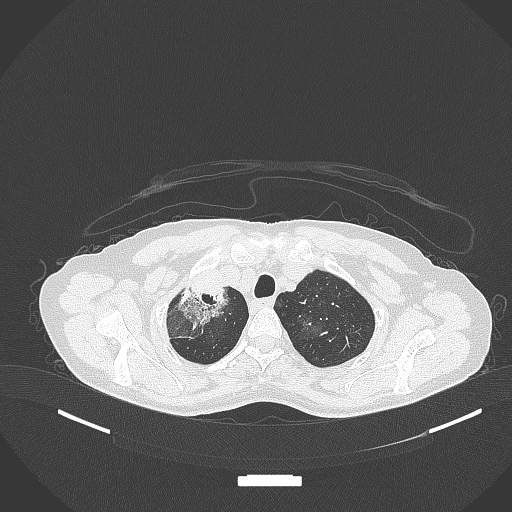
Chest CT, one axial slice; position 280 of 284 along the scan axis; reconstruction kernel B70f; lung window (W 1500 / L -600 HU); 512 × 512 image matrix. Female patient, age 59 years. Case-level facts recorded for this patient, not image findings: clinical TNM (as recorded): T3 N0 M0; histopathological grade: G1.
Structures marked on this image (bounding box drawn by a radiologist):
- lung tumour (recorded histology: adenocarcinoma): box from (x=173, y=281) to (x=228, y=325) px